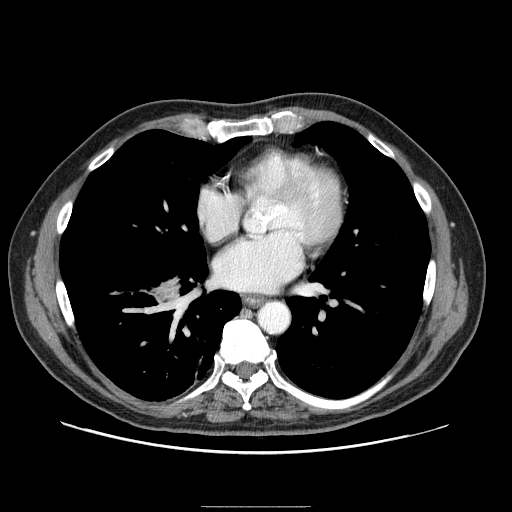
Contrast-enhanced abdominal CT (liver protocol), one axial slice. Position 92 of 99 along the scan axis. Reconstruction kernel STANDARD. 100 kVp. One of 2 acquisitions stored at this slice position. Soft-tissue window (W 400 / L 40 HU). 2.5 mm slice thickness. 512 × 512 image matrix. From the clinical record (not read from this slice): diagnosis: hepatocellular carcinoma (patient treated with transarterial chemoembolisation; whether this scan precedes or follows treatment is not stated here); TNM stage (as recorded): Stage-II; Child-Pugh class: A; tumour differentiation: well differentiated; tumour nodularity: multinodular.
Outlined on this slice (semi-automatic segmentation, software-assisted and operator-edited):
- liver parenchyma outside the tumour (the mass and vessels are separate outlines, so this box may not span the whole liver): bounding box [x1, y1, x2, y2] px = [158, 286, 176, 302]